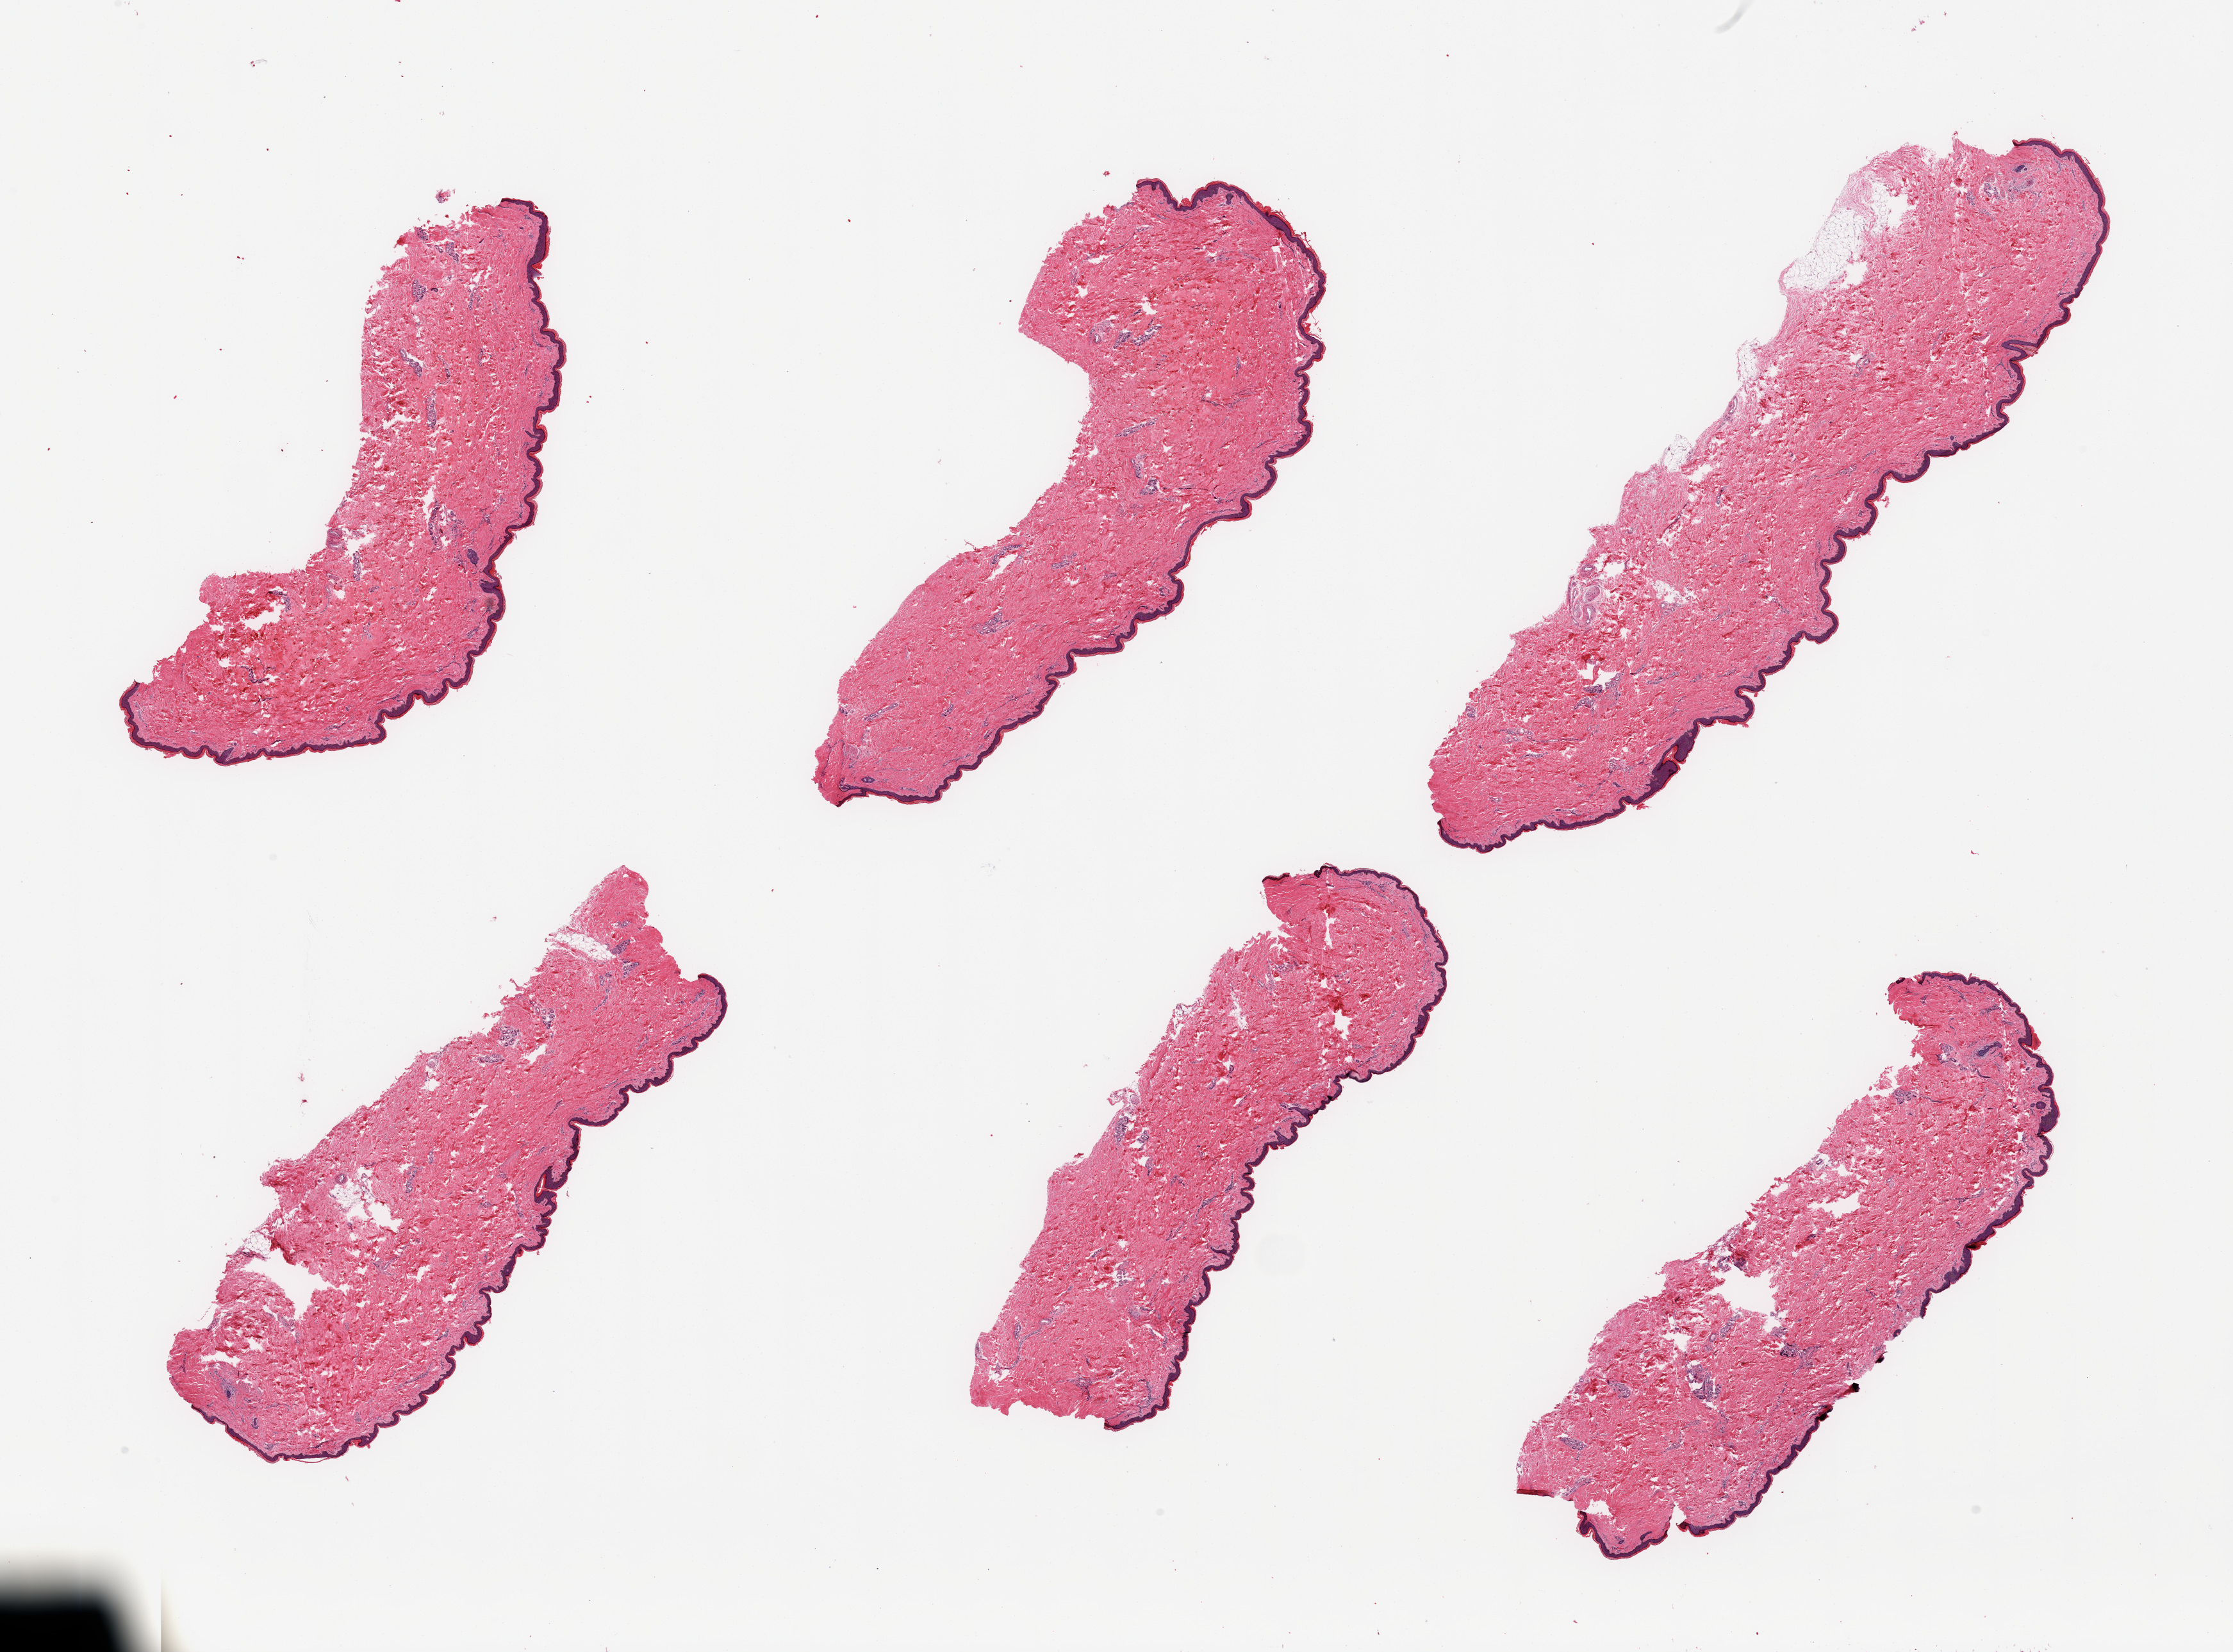
Digitized hematoxylin and eosin (H&E)-stained section, shown as a low-resolution overview of the whole scanned area (about 27.6 x 20.4 mm), PAXgene-fixed paraffin-embedded (PFPE) section, target tissue: skin of lower leg, tissue donor sample. Donor: male.
Review note (as recorded): 6 pieces; <2% dermal fat; well trimmed.